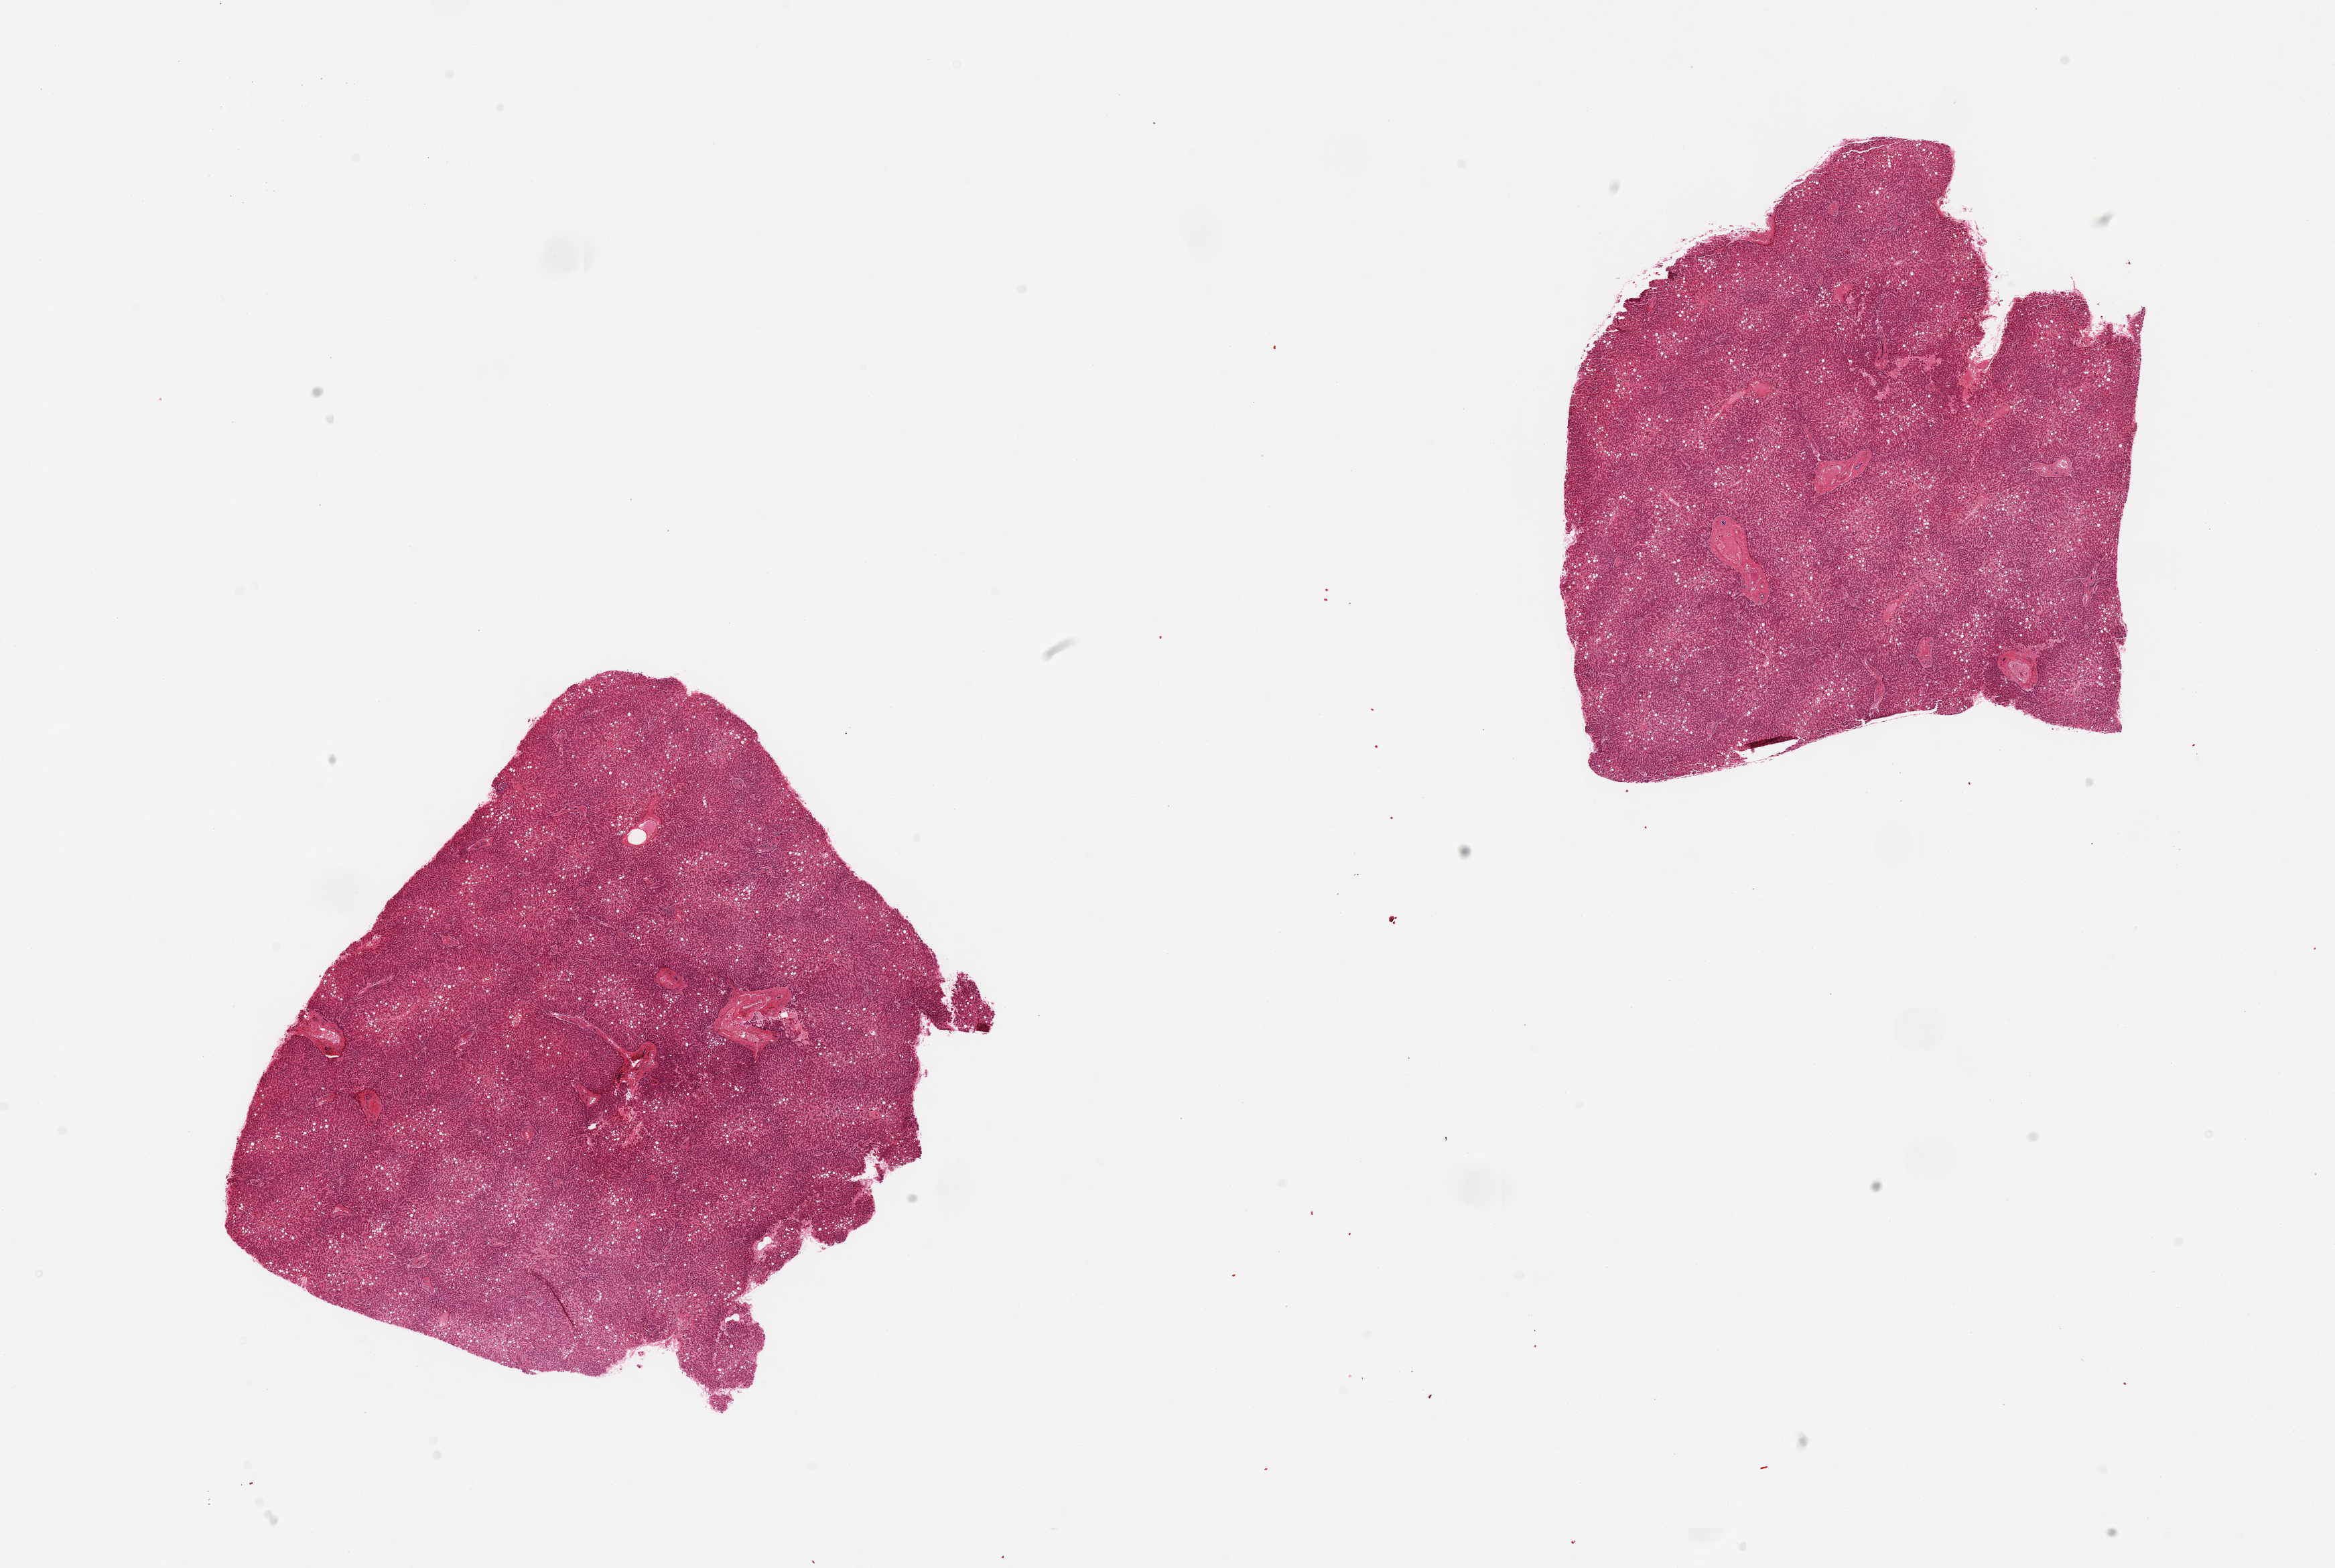
Digitized haematoxylin and eosin-stained section, a low-resolution overview of the entire scanned area, about 27.6 x 18.5 mm; PAXgene-fixed, paraffin-embedded tissue; section of liver (target tissue); donor tissue sample.
- pathologist's review note for this sample: 2 pieces, mild to moderate steatosis